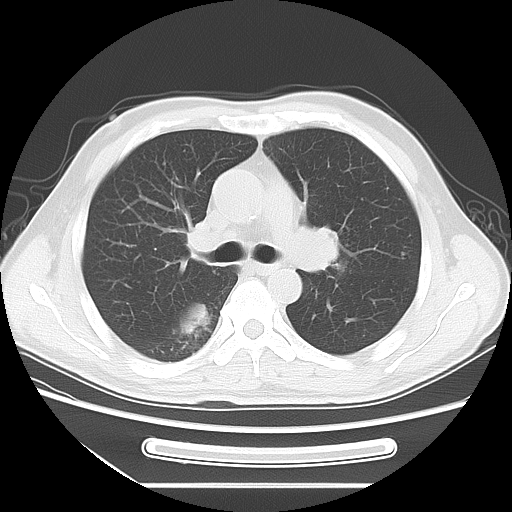
Chest CT, one axial slice; slice 46 of 71 in the series (ordered by position); 120 kVp; lung window (W 1500 / L -600 HU); 5 mm slice thickness; 512 × 512 image matrix, field of view 366 × 366 mm. Male patient, age 51 years. From the clinical record (not read from this slice): clinical TNM (as recorded): T1c N3 M0.
Structures marked on this image (rectangle marked by the reading radiologist):
- lung tumour (recorded histology: adenocarcinoma): bounding box <289,213,353,286> (left, top, right, bottom; pixels)